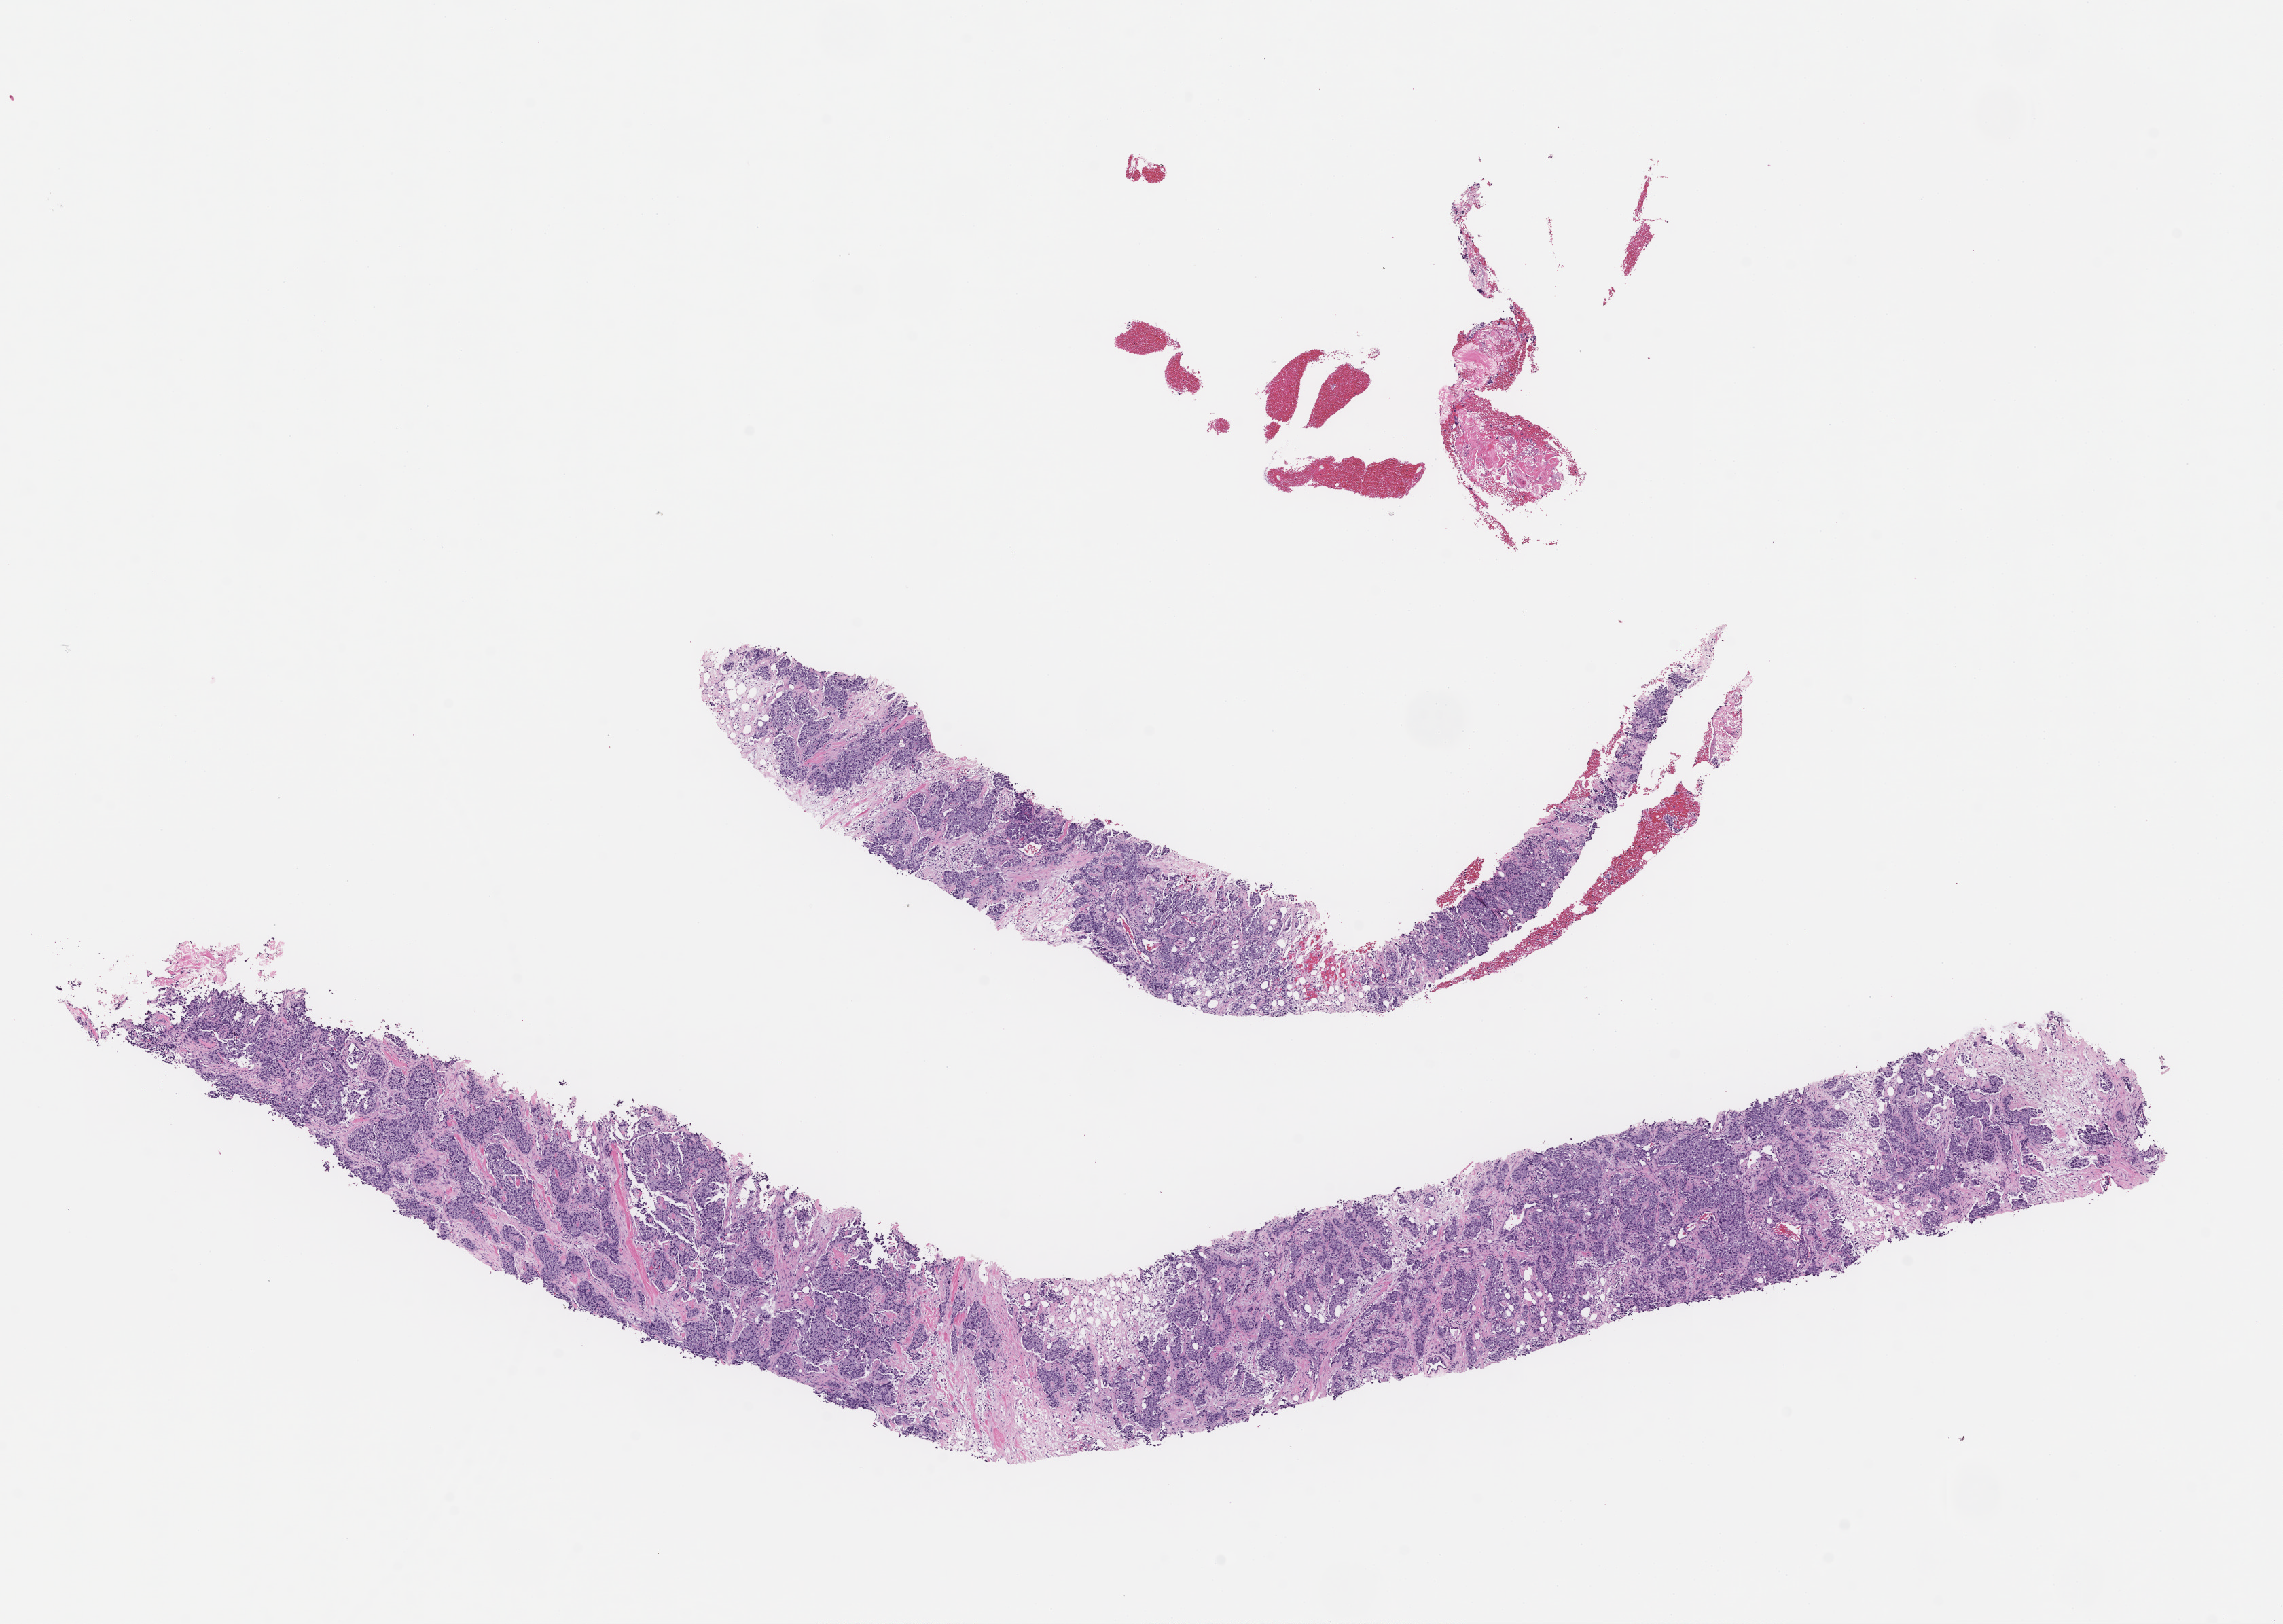
Haematoxylin and eosin whole-slide image, a low-resolution overview of the entire scanned area, about 13.6 x 9.7 mm; formalin-fixed, paraffin-embedded (FFPE) tissue; tissue site: breast. Female patient.
This section: primary tumor. Diagnosis: Invasive Breast Carcinoma.